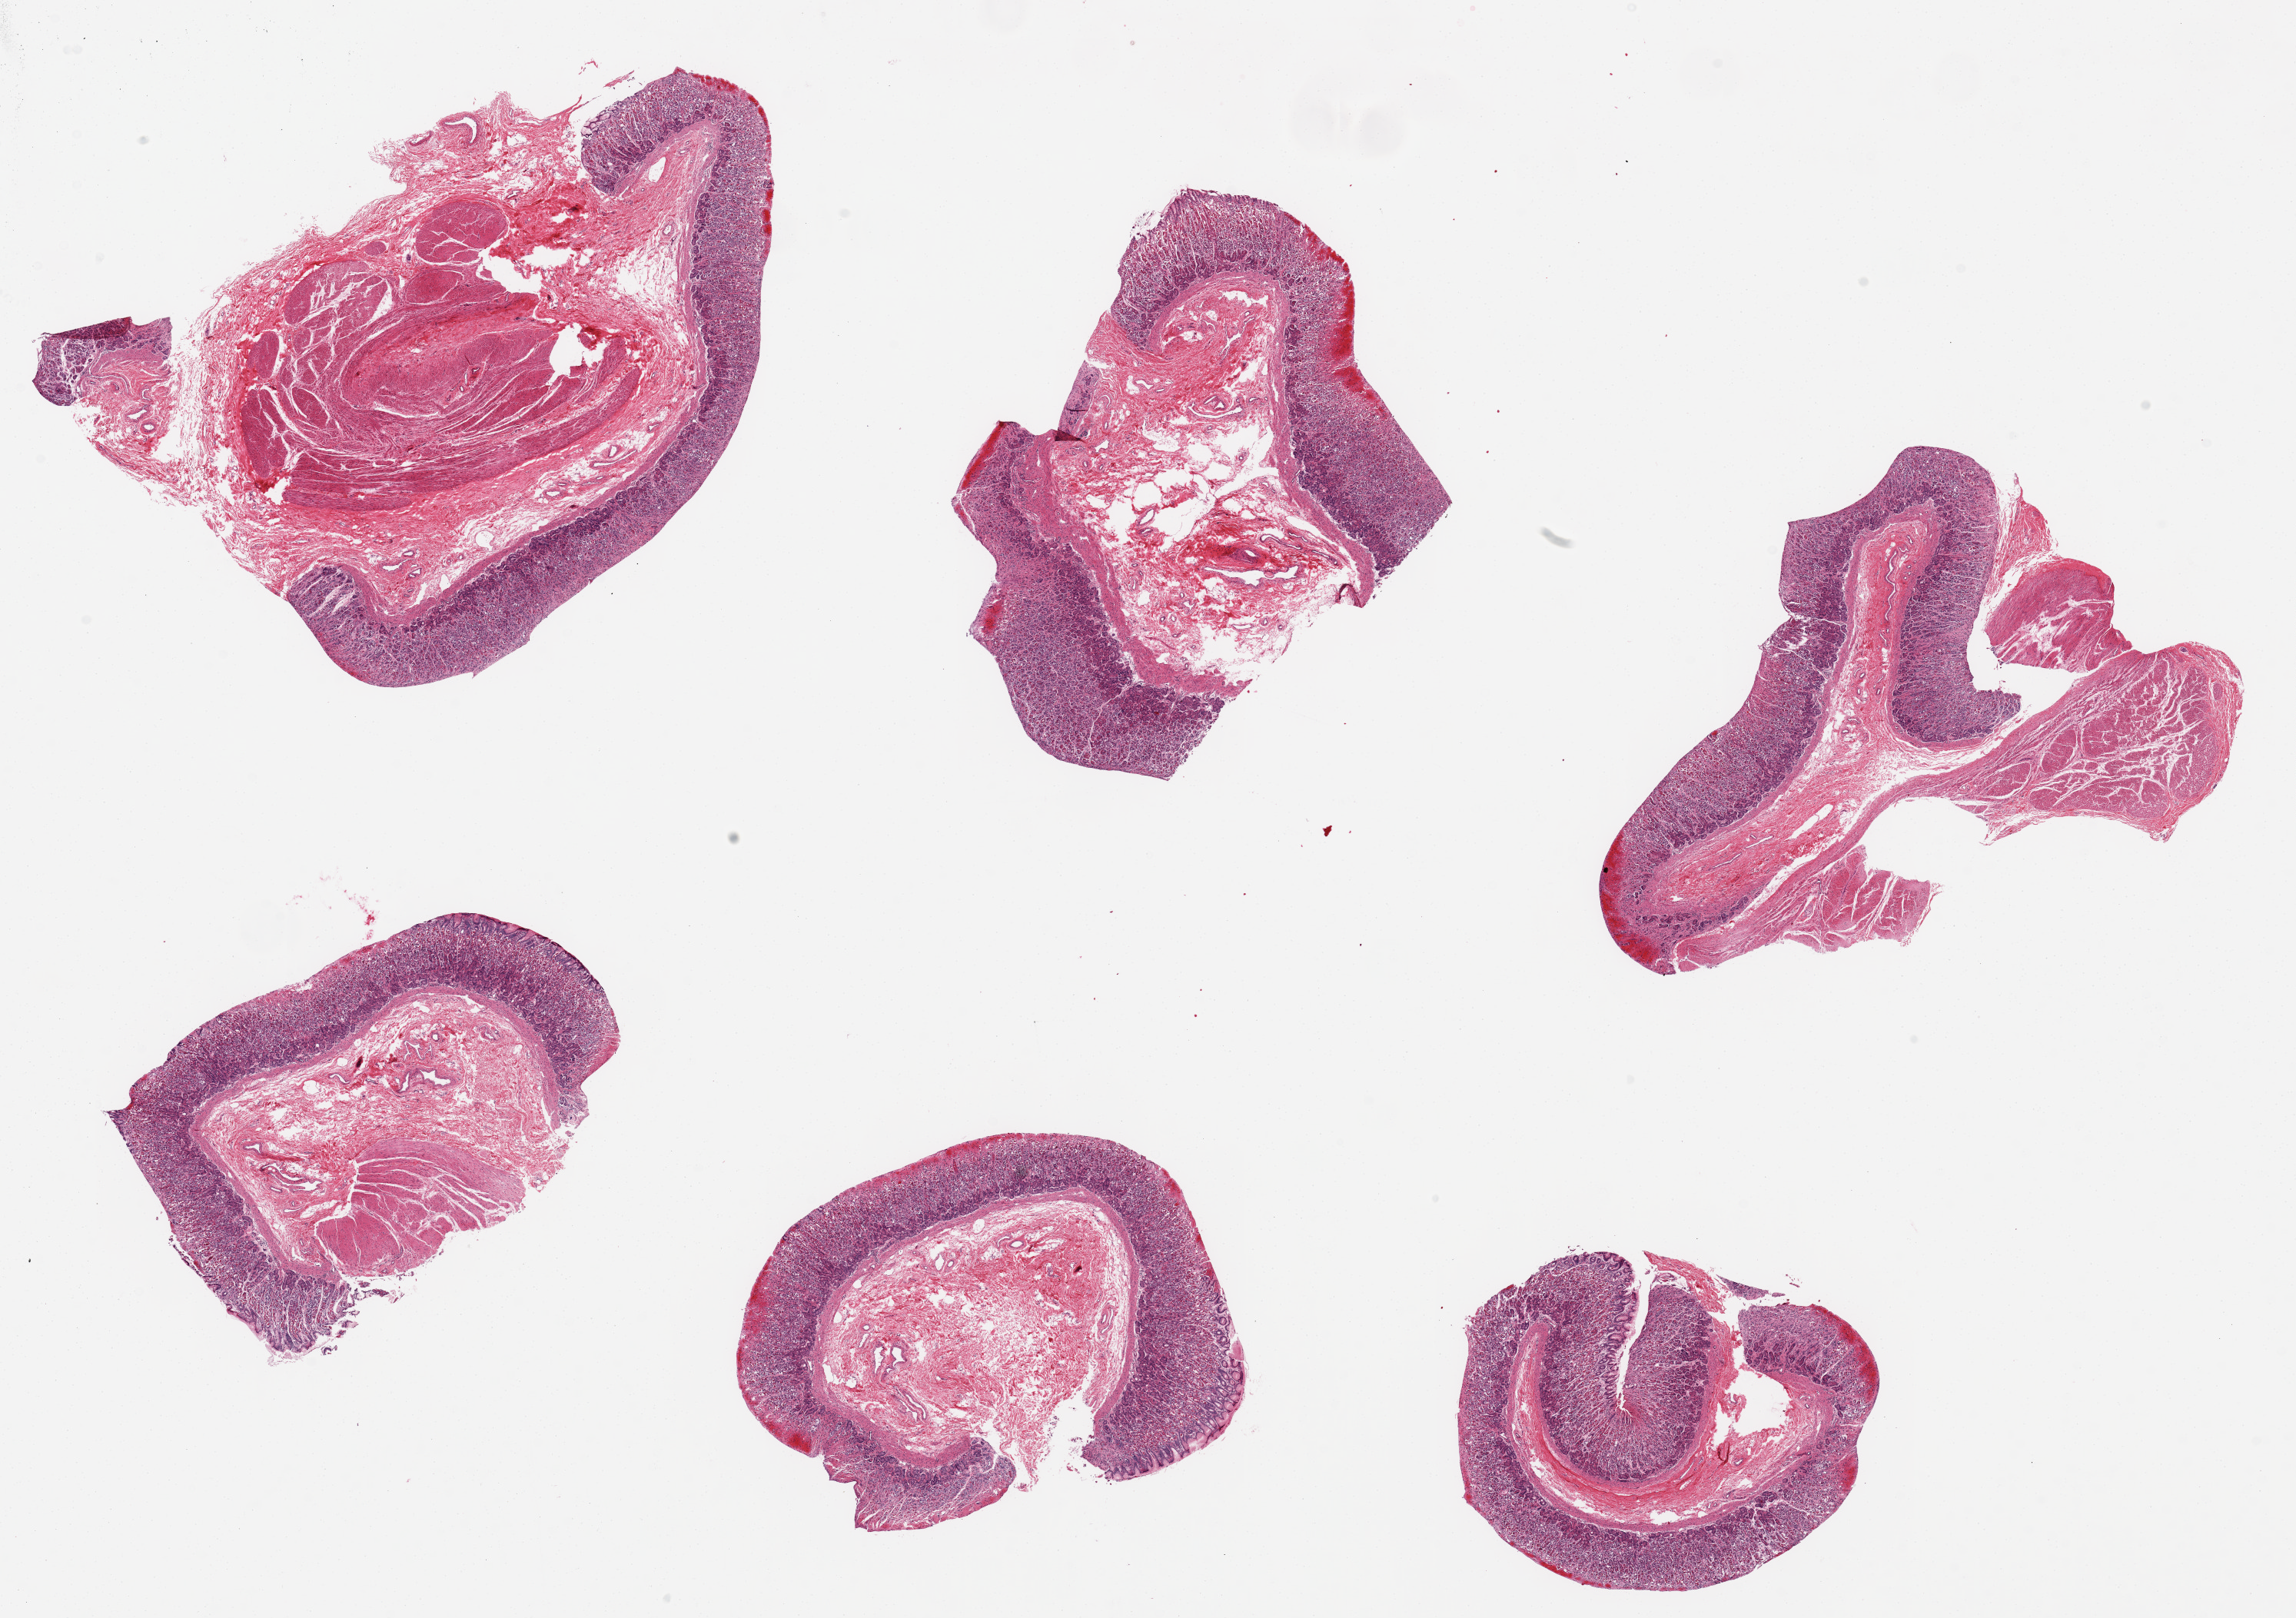
Whole-slide image, H&E stain, brightfield, low-resolution overview of the scanned area, about 23.6 x 16.6 mm (acquisition: 20x scan); PAXgene-fixed, paraffin-embedded tissue; sampled site (target tissue): stomach; donor tissue sample. Donor sex: male.
Pathologist's review note for this sample: 6 pieces up to ~7x5 mm; mucosa largely autolyzed; focal mucosal surface hemorrhages.